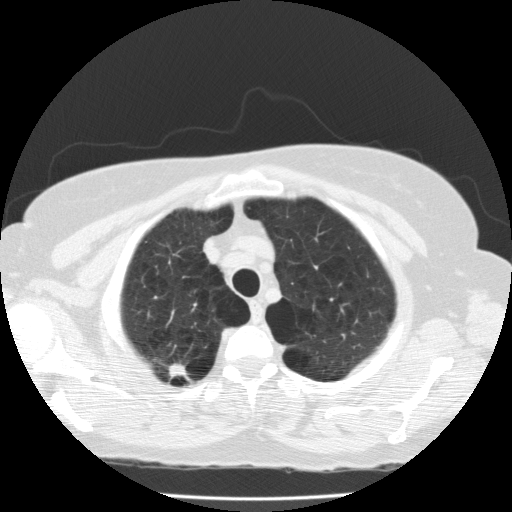
Chest CT (low-dose screening protocol), one axial image; second screening round (one year after baseline); lung window (W 1500 / L -600 HU); slice 26 of 174 in the series. Female, age 59 years at enrolment.
- Expert-annotated lung lesion, box from (x=142, y=348) to (x=198, y=393) px.
- Reader record for this screening exam (exam-level; its link to the box is not recorded): non-calcified nodule or mass ≥4 mm, right upper lobe, 11 × 6 mm, spiculated (stellate) margins, soft tissue attenuation, pre-existing on the prior screen: yes; interval growth: no.
- Official screen result: positive, no significant change: stable abnormalities potentially related to lung cancer, unchanged since the prior screening exam.
- Lung cancer was diagnosed 490 days after this screen: adenocarcinoma, NOS, right upper lobe, poorly differentiated (G3), stage IA (AJCC 6th edition), 20 mm at pathology.